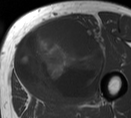
MRI of an extremity soft-tissue mass, one axial slice; slice 36 of 55 in the series (ordered by position); MR volume resampled by the dataset authors to the PET/CT grid (not the native acquisition matrix); 131 × 118 image matrix, field of view 128 × 115 mm. Male patient. From the clinical record (not read from this slice): histological type: pleiomorphic liposarcoma; grade: high; site of the primary tumour: left thigh.
Structures marked on this image (expert contour drawn on MRI and transferred to this co-registered scan by the dataset authors):
- gross tumour volume including surrounding oedema: bounding box <14,18,106,101> (left, top, right, bottom; pixels)
- gross tumour volume (mass): <14,18,103,101>